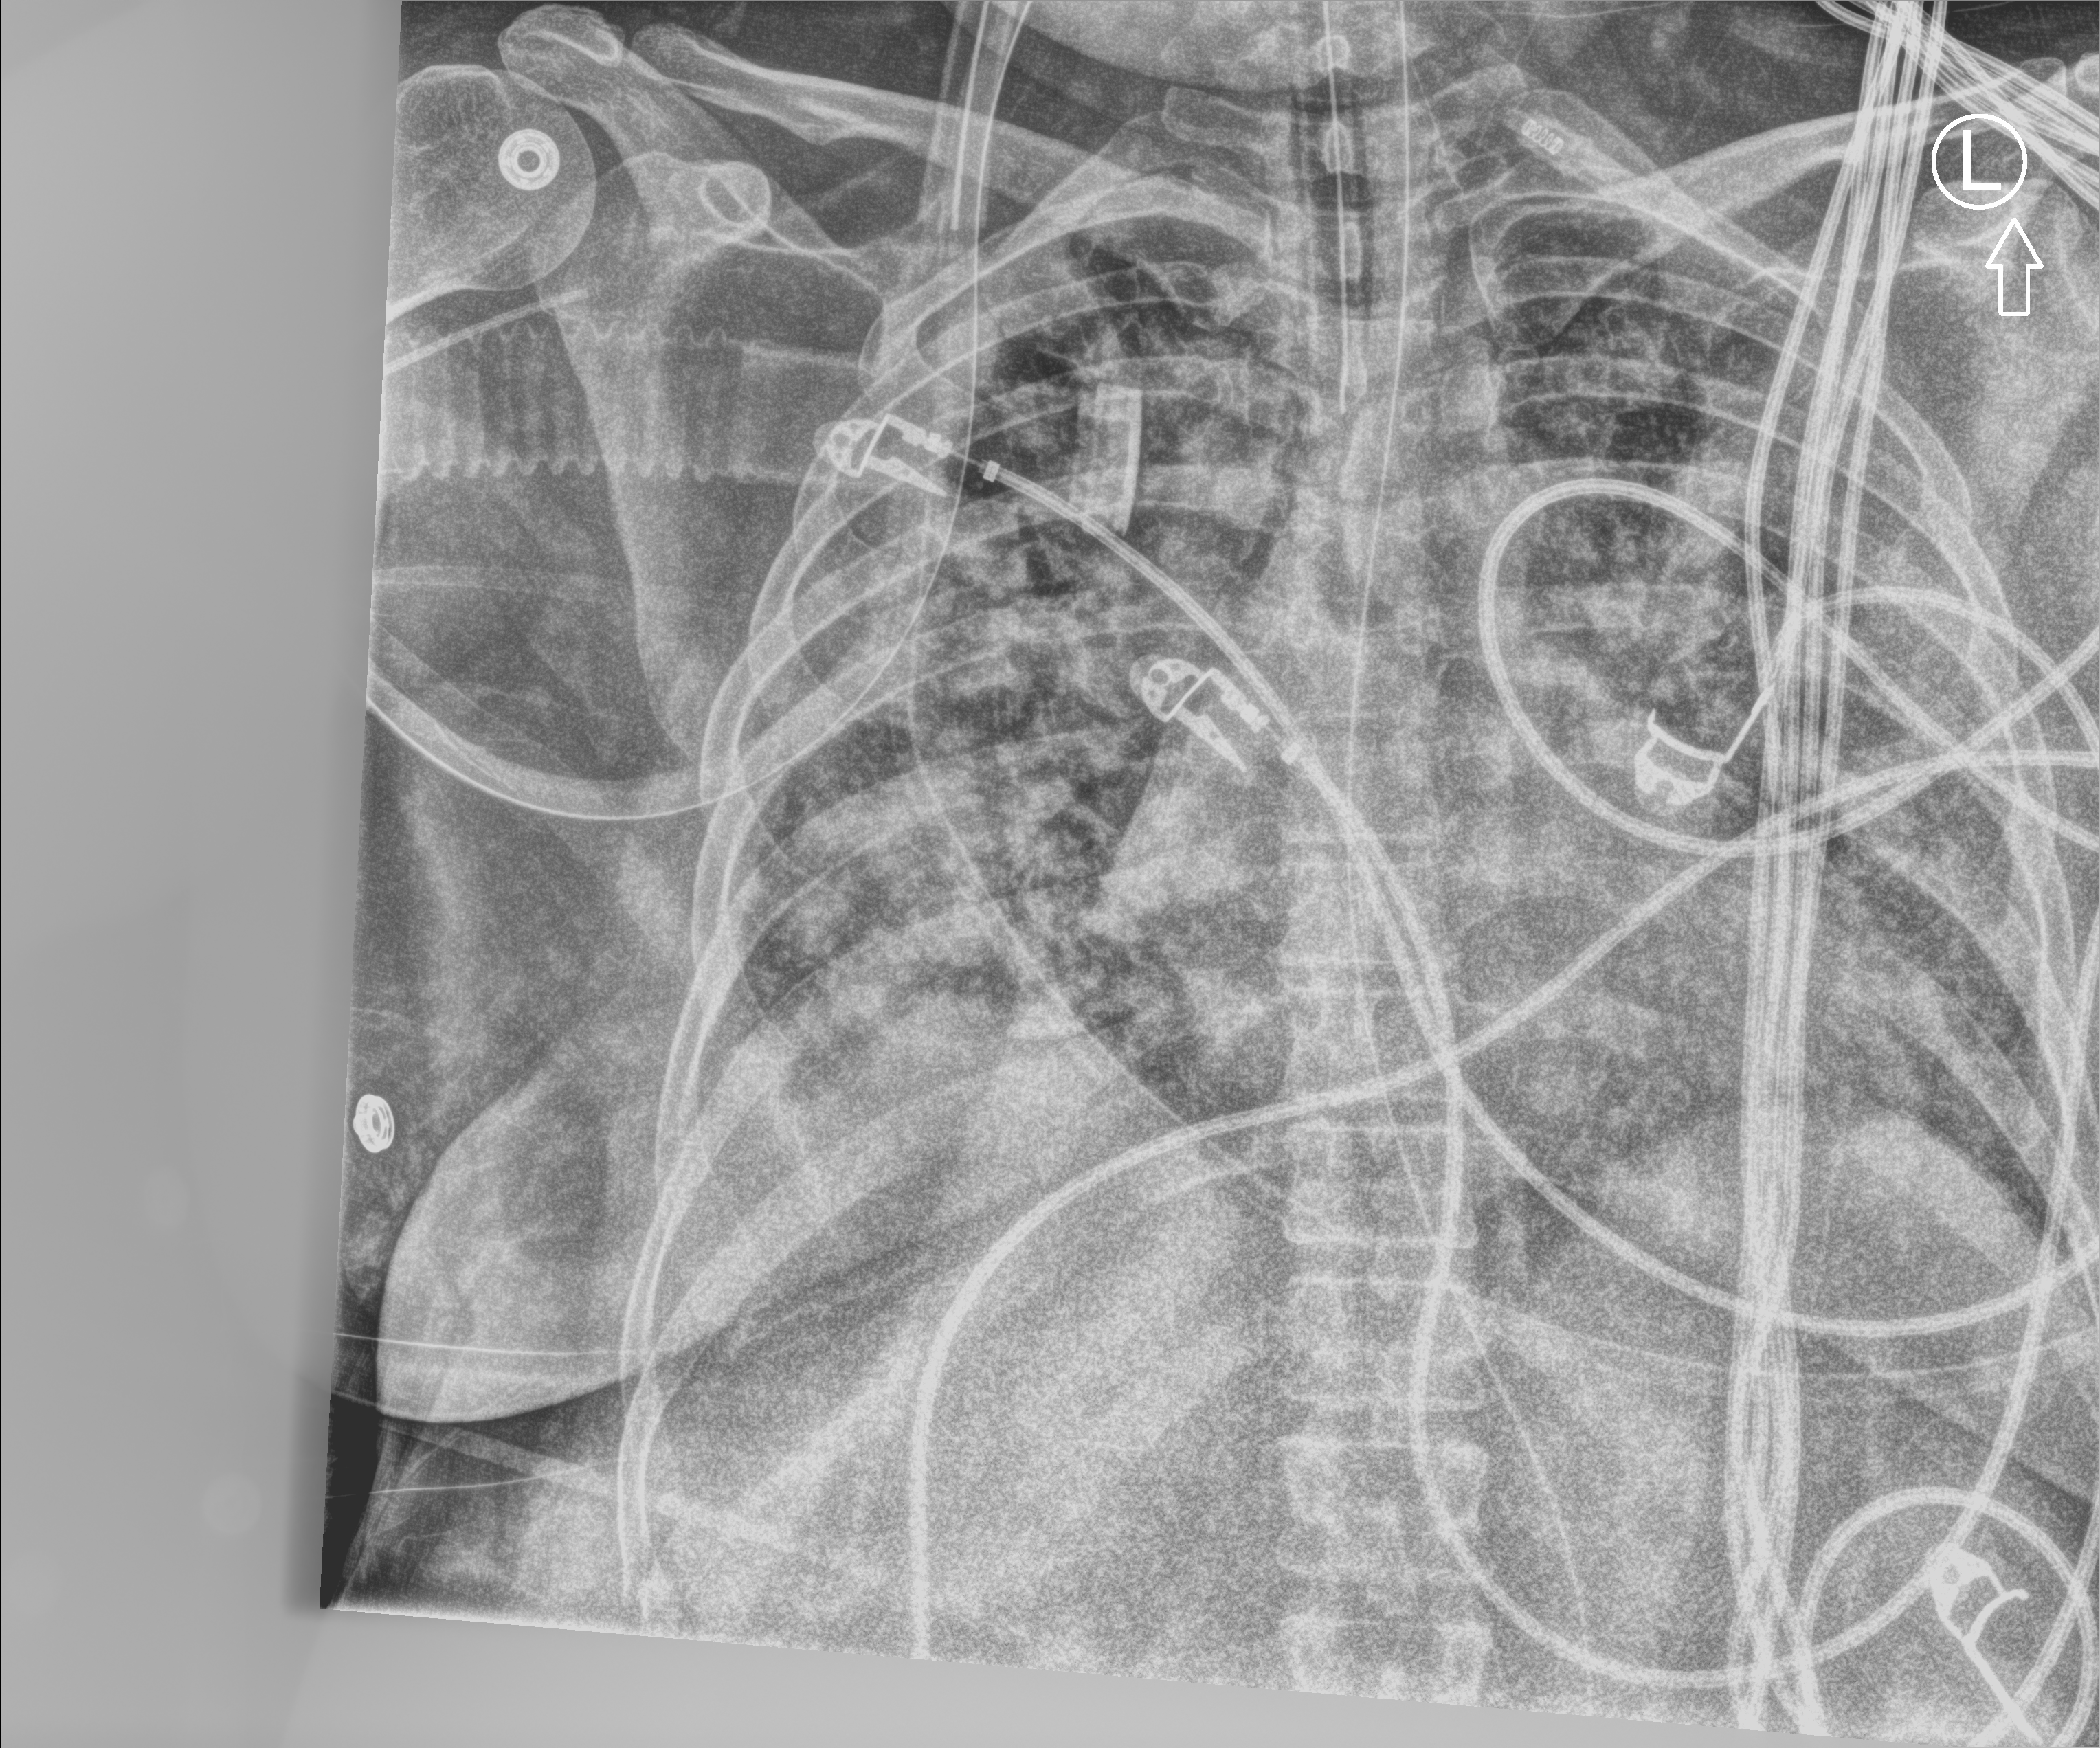
Chest X-ray (portable). Patient hospitalised with COVID-19; female, aged 18–59 years.
Admission-level facts for this patient (not findings on this image; timing relative to this image not recorded): mechanically ventilated during this hospital stay: yes.